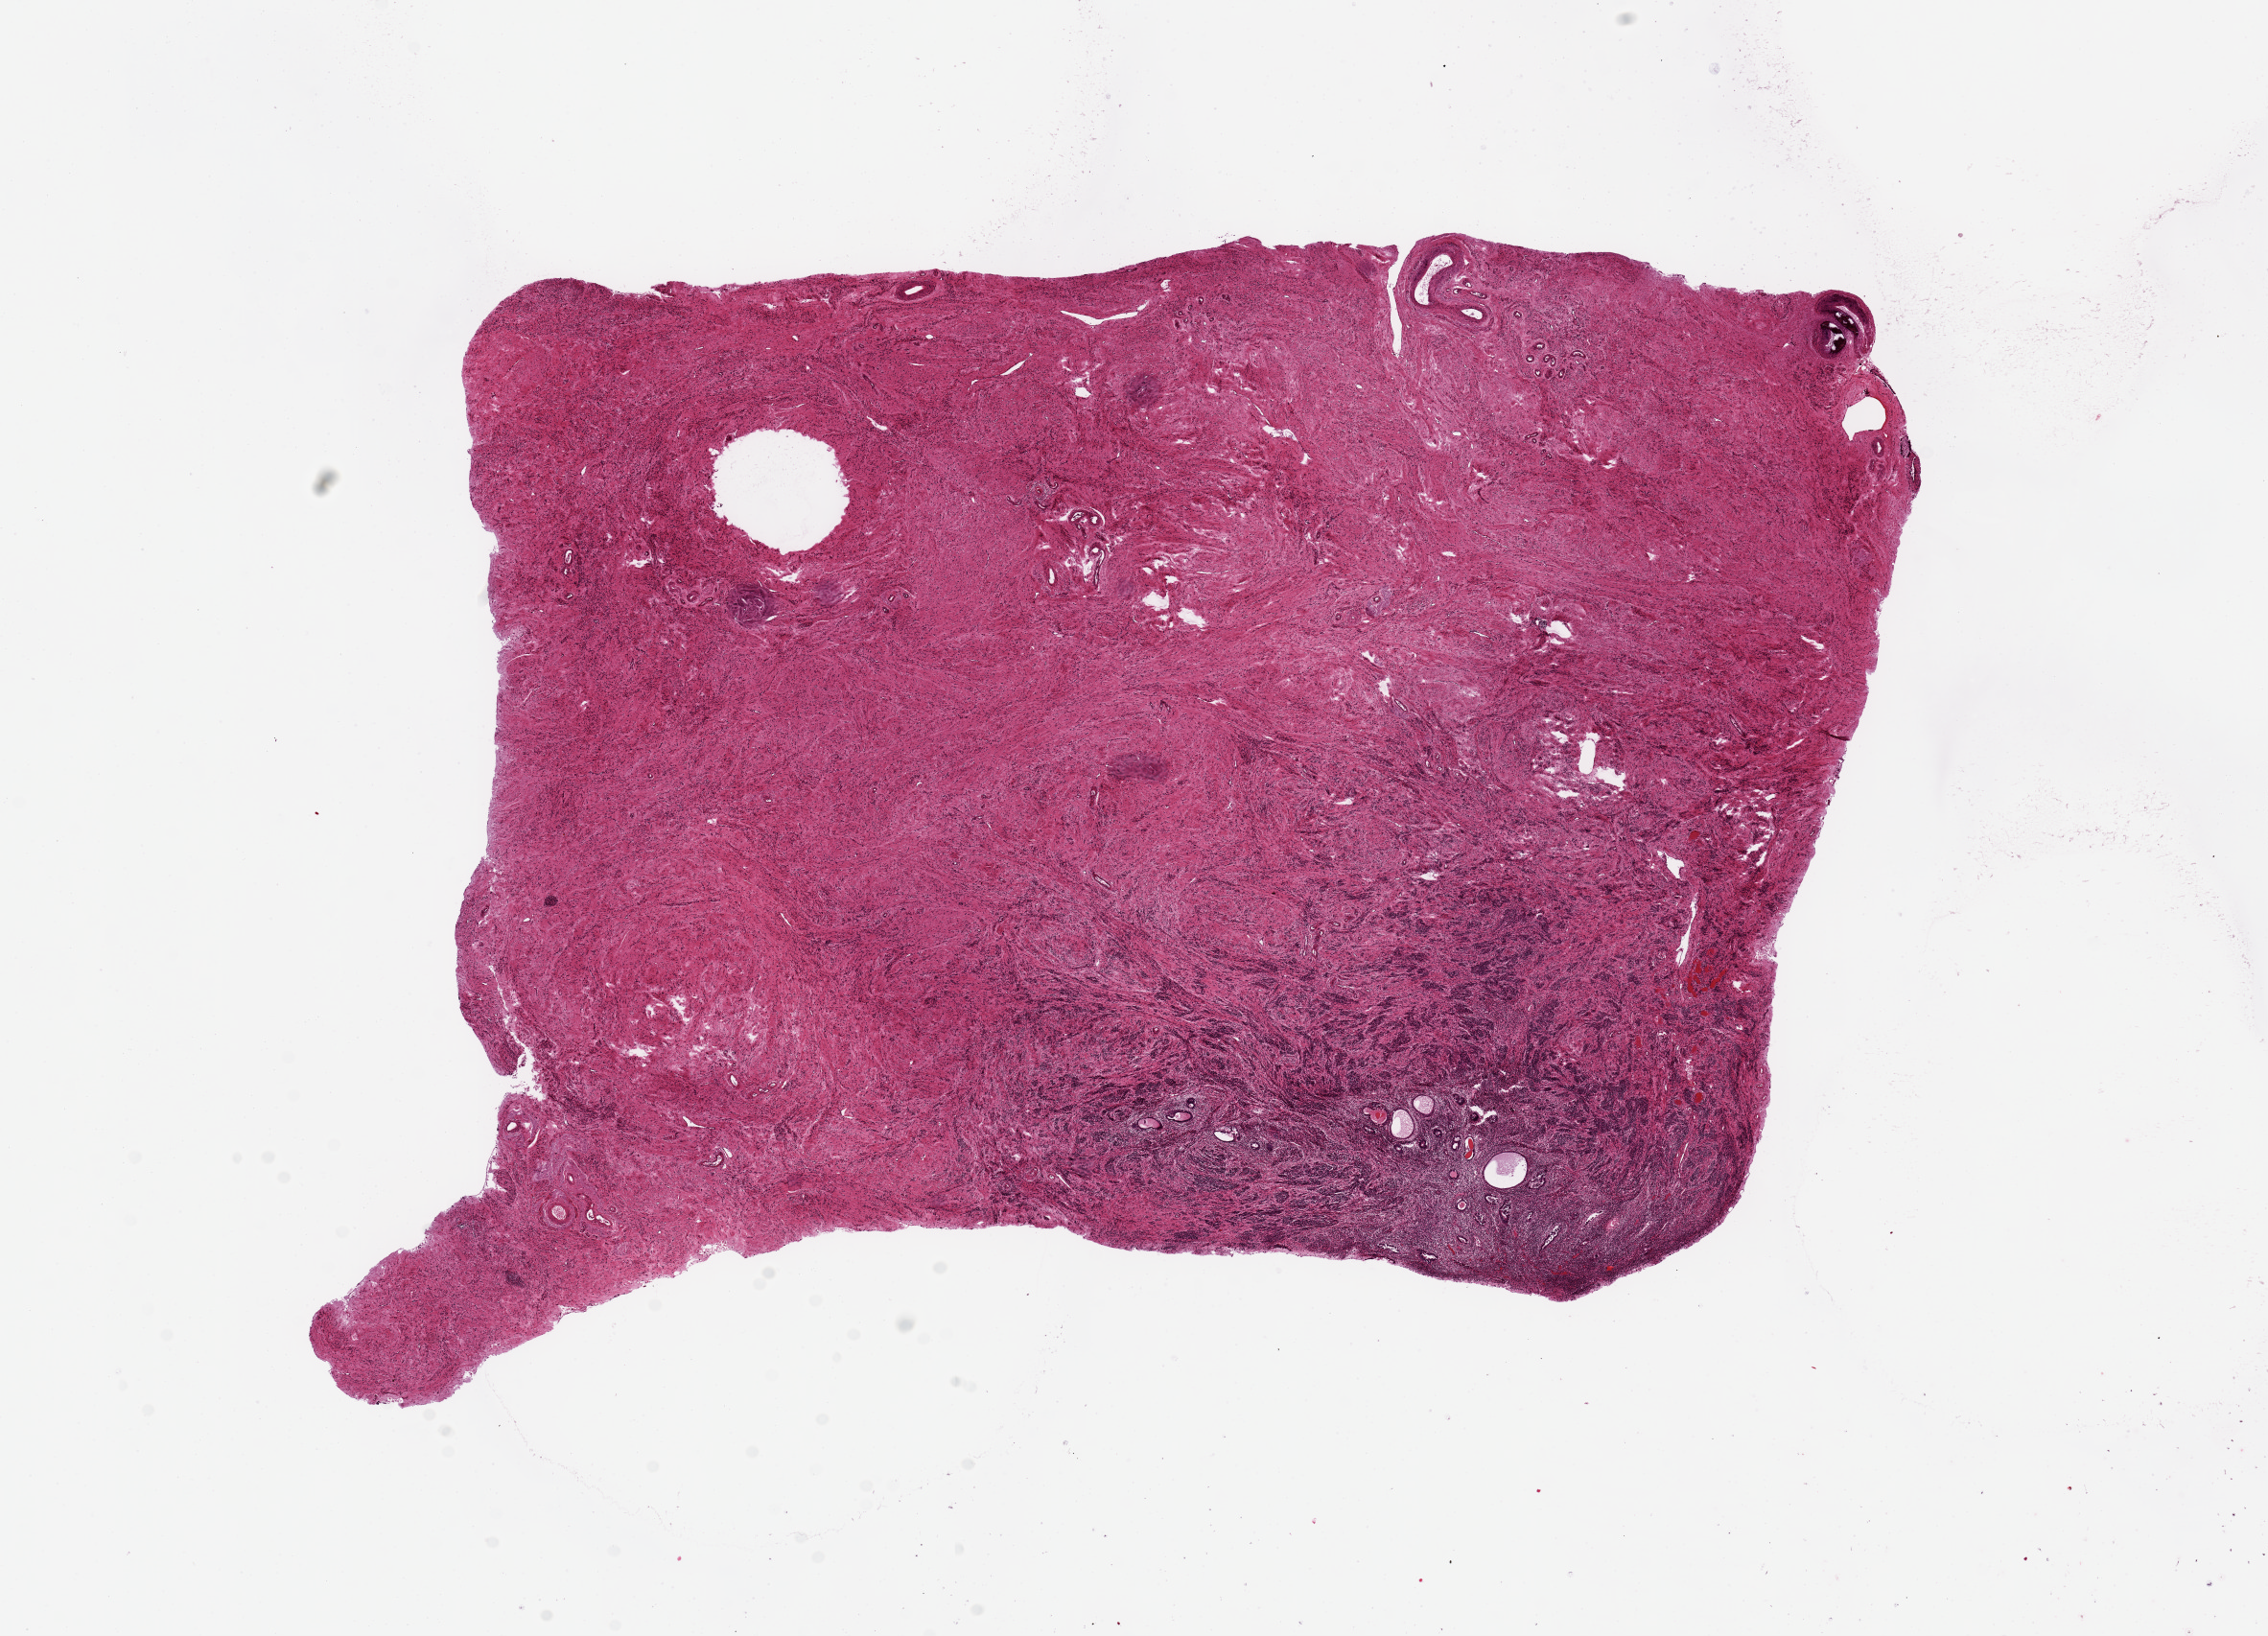
Hematoxylin and eosin (H&E) whole-slide image, brightfield, low-resolution overview of the scanned area, about 18.7 x 13.5 mm. PAXgene-fixed, paraffin-embedded tissue. Sampled site (target tissue): uterus. Tissue donor sample. Female donor.
Reviewer comment on this tissue sample: 11x8 mm; atrophic endometrium, calcified arteries.